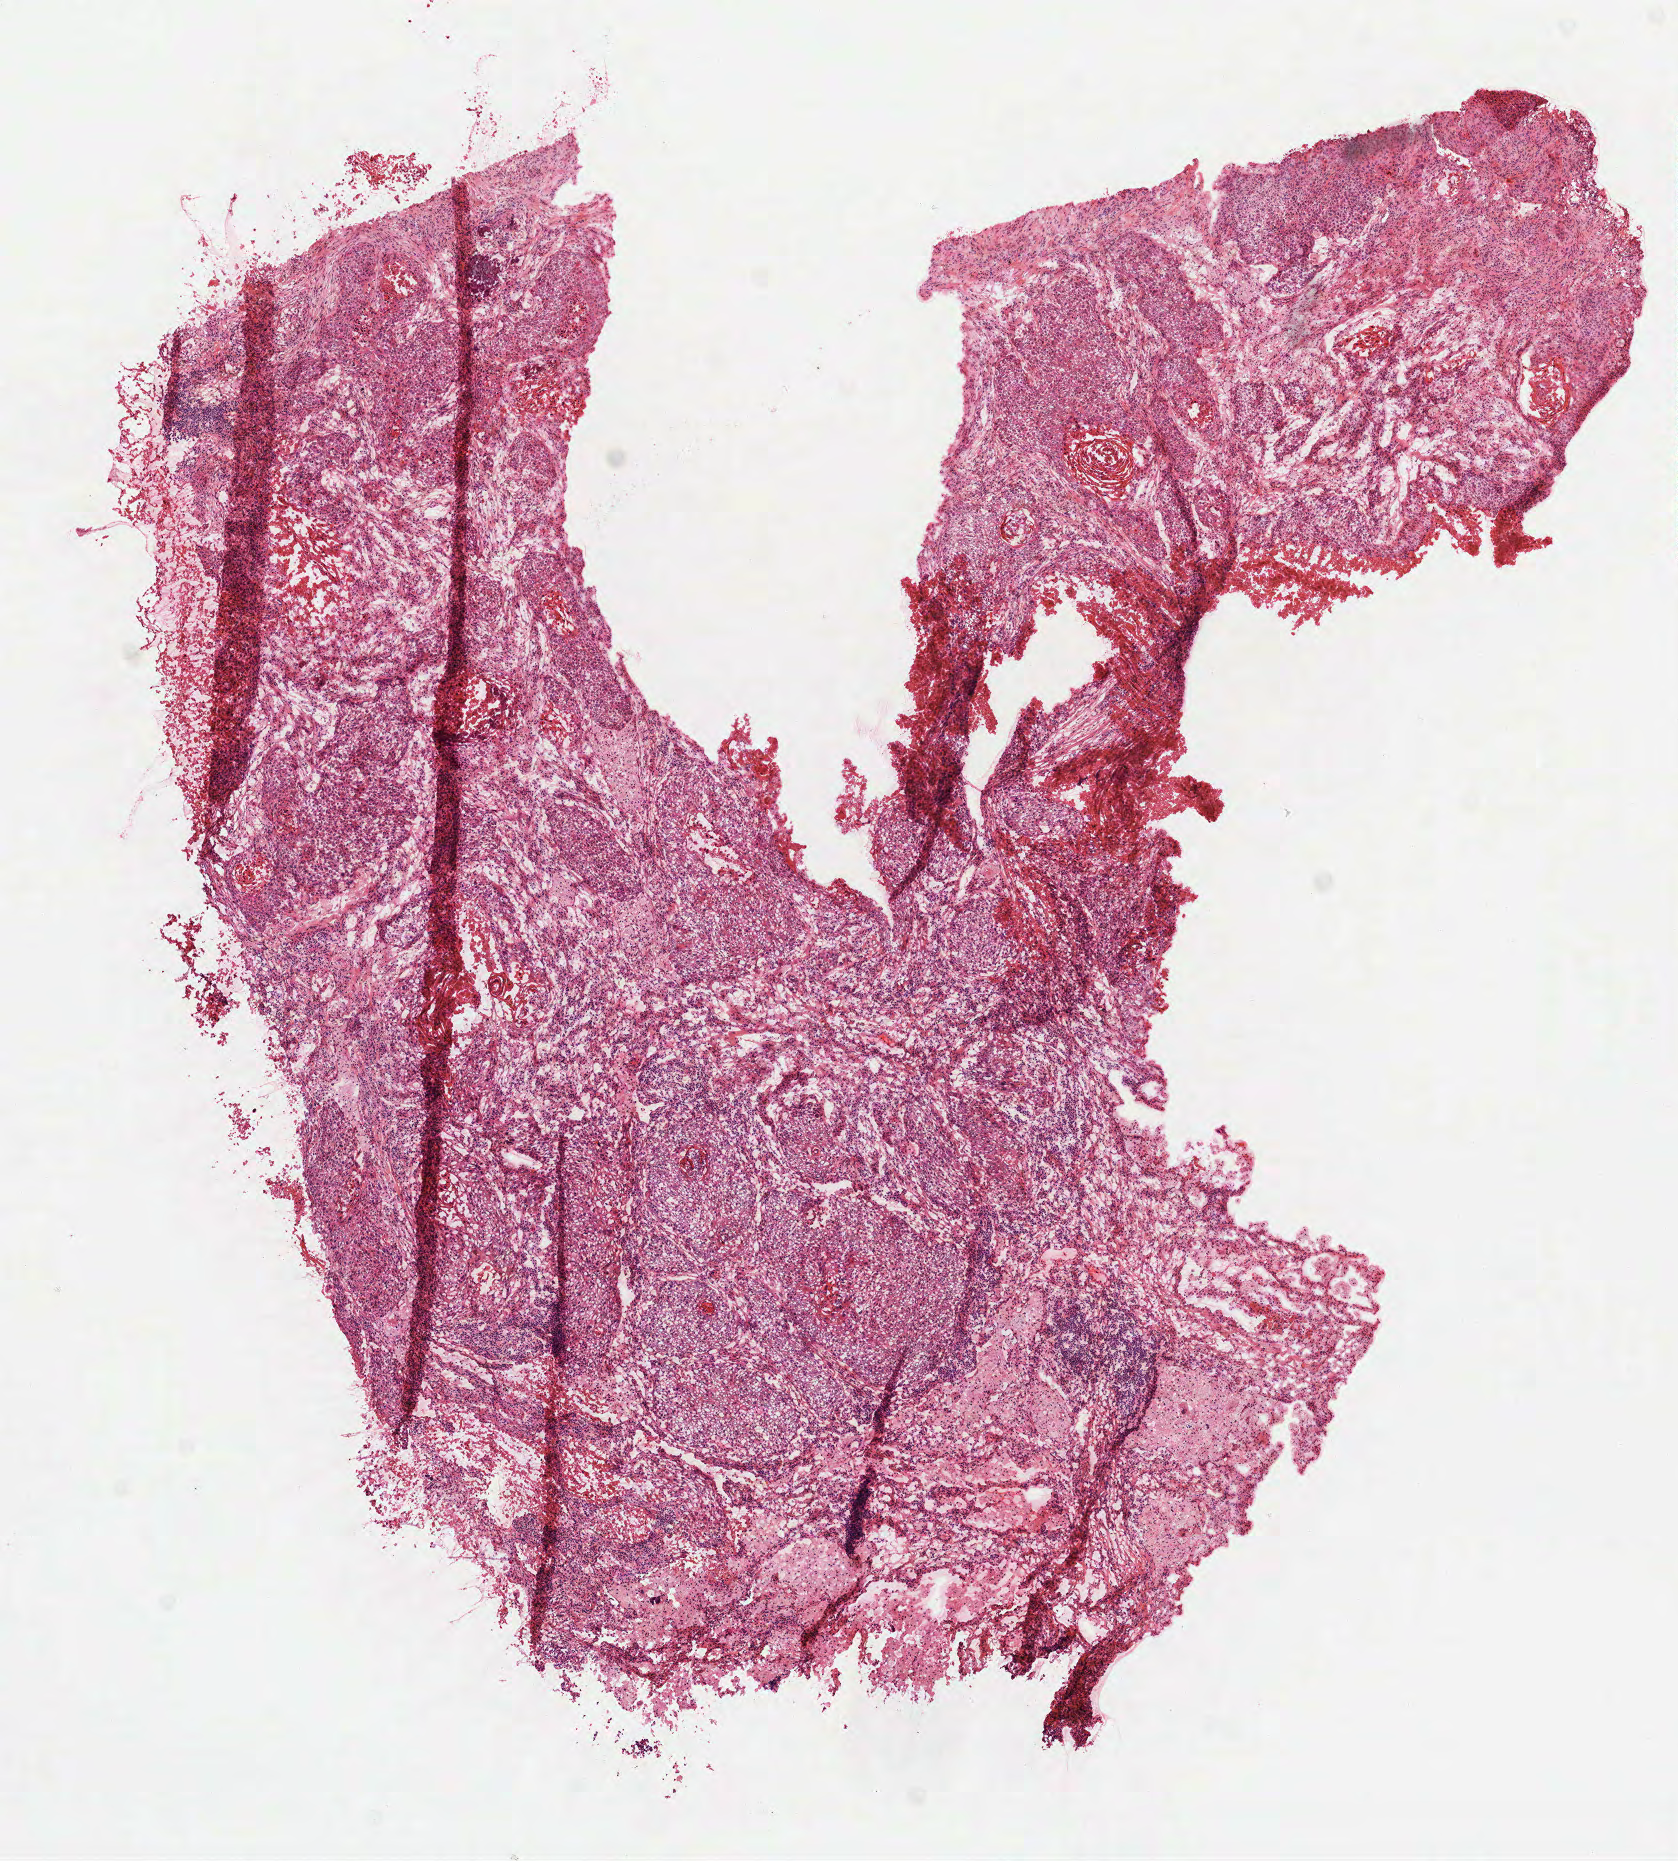
Hematoxylin and eosin (H&E) stained whole-slide image, whole scanned area (about 6.8 x 7.5 mm) shown as a low-resolution overview; formalin-fixed paraffin-embedded (FFPE) diagnostic section; lung, primary tumour sample. Female patient; age at initial diagnosis 54 years.
• diagnosis: Squamous cell carcinoma, NOS (lower lobe, lung)
• AJCC pathologic stage: IB
• TNM: T2 N0 M0